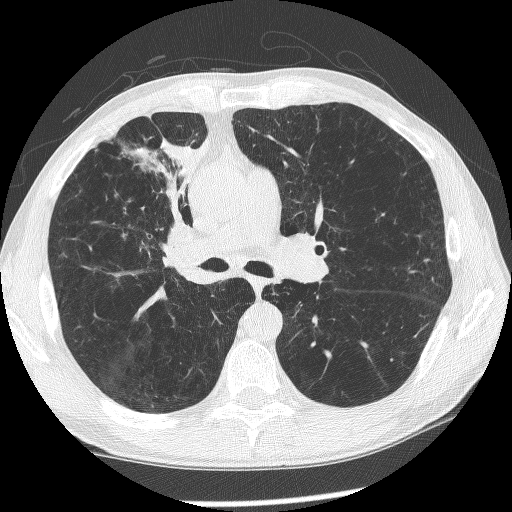
Low-dose screening chest CT, axial slice, baseline annual screen, lung window (W 1500 / L -600 HU), 1.25 mm slice thickness, lung (sharp) reconstruction kernel (BONE). Male, age 60 years at enrolment. Current smoker at enrolment.
• Lesion marked by an expert reader, bounding box <145,192,220,285> (left, top, right, bottom; pixels).
• The exam's reader record, not a measurement of the box and not confirmed to be the same lesion: non-calcified nodule or mass ≥4 mm, right upper lobe, 12 × 8 mm, spiculated (stellate) margins, mixed attenuation.
• Lung cancer was diagnosed 208 days after this screen: squamous cell carcinoma, NOS, right upper lobe, right middle lobe, right main stem bronchus, poorly differentiated (G3), stage IV (AJCC 6th edition).